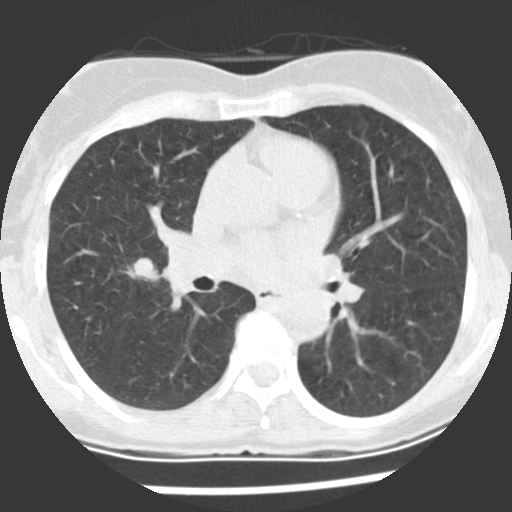
Low-dose screening chest CT, axial slice. First (baseline) screen. Lung window (W 1500 / L -600 HU). Standard (soft-tissue) reconstruction kernel (STANDARD). Slice 106 of 225 in the series. 512 × 512 image matrix. Female, age 60 years at enrolment. Current smoker at enrolment.
• Lesion marked by an expert reader, bounding box (x1, y1, x2, y2) in pixels: (116, 251, 174, 296).
• The screening reader recorded 2 non-calcified nodules or masses ≥4 mm on this exam; which of them this box marks is not recorded.
• Official screen result: positive, change unspecified: nodule(s) >= 4 mm or enlarging nodule(s), mass(es), or other non-specific abnormalities suspicious for lung cancer.
• Participant outcome: lung cancer diagnosed 10 days after this screen — adenocarcinoma, NOS, right upper lobe, stage IIIA (AJCC 6th edition), 20 mm at pathology.